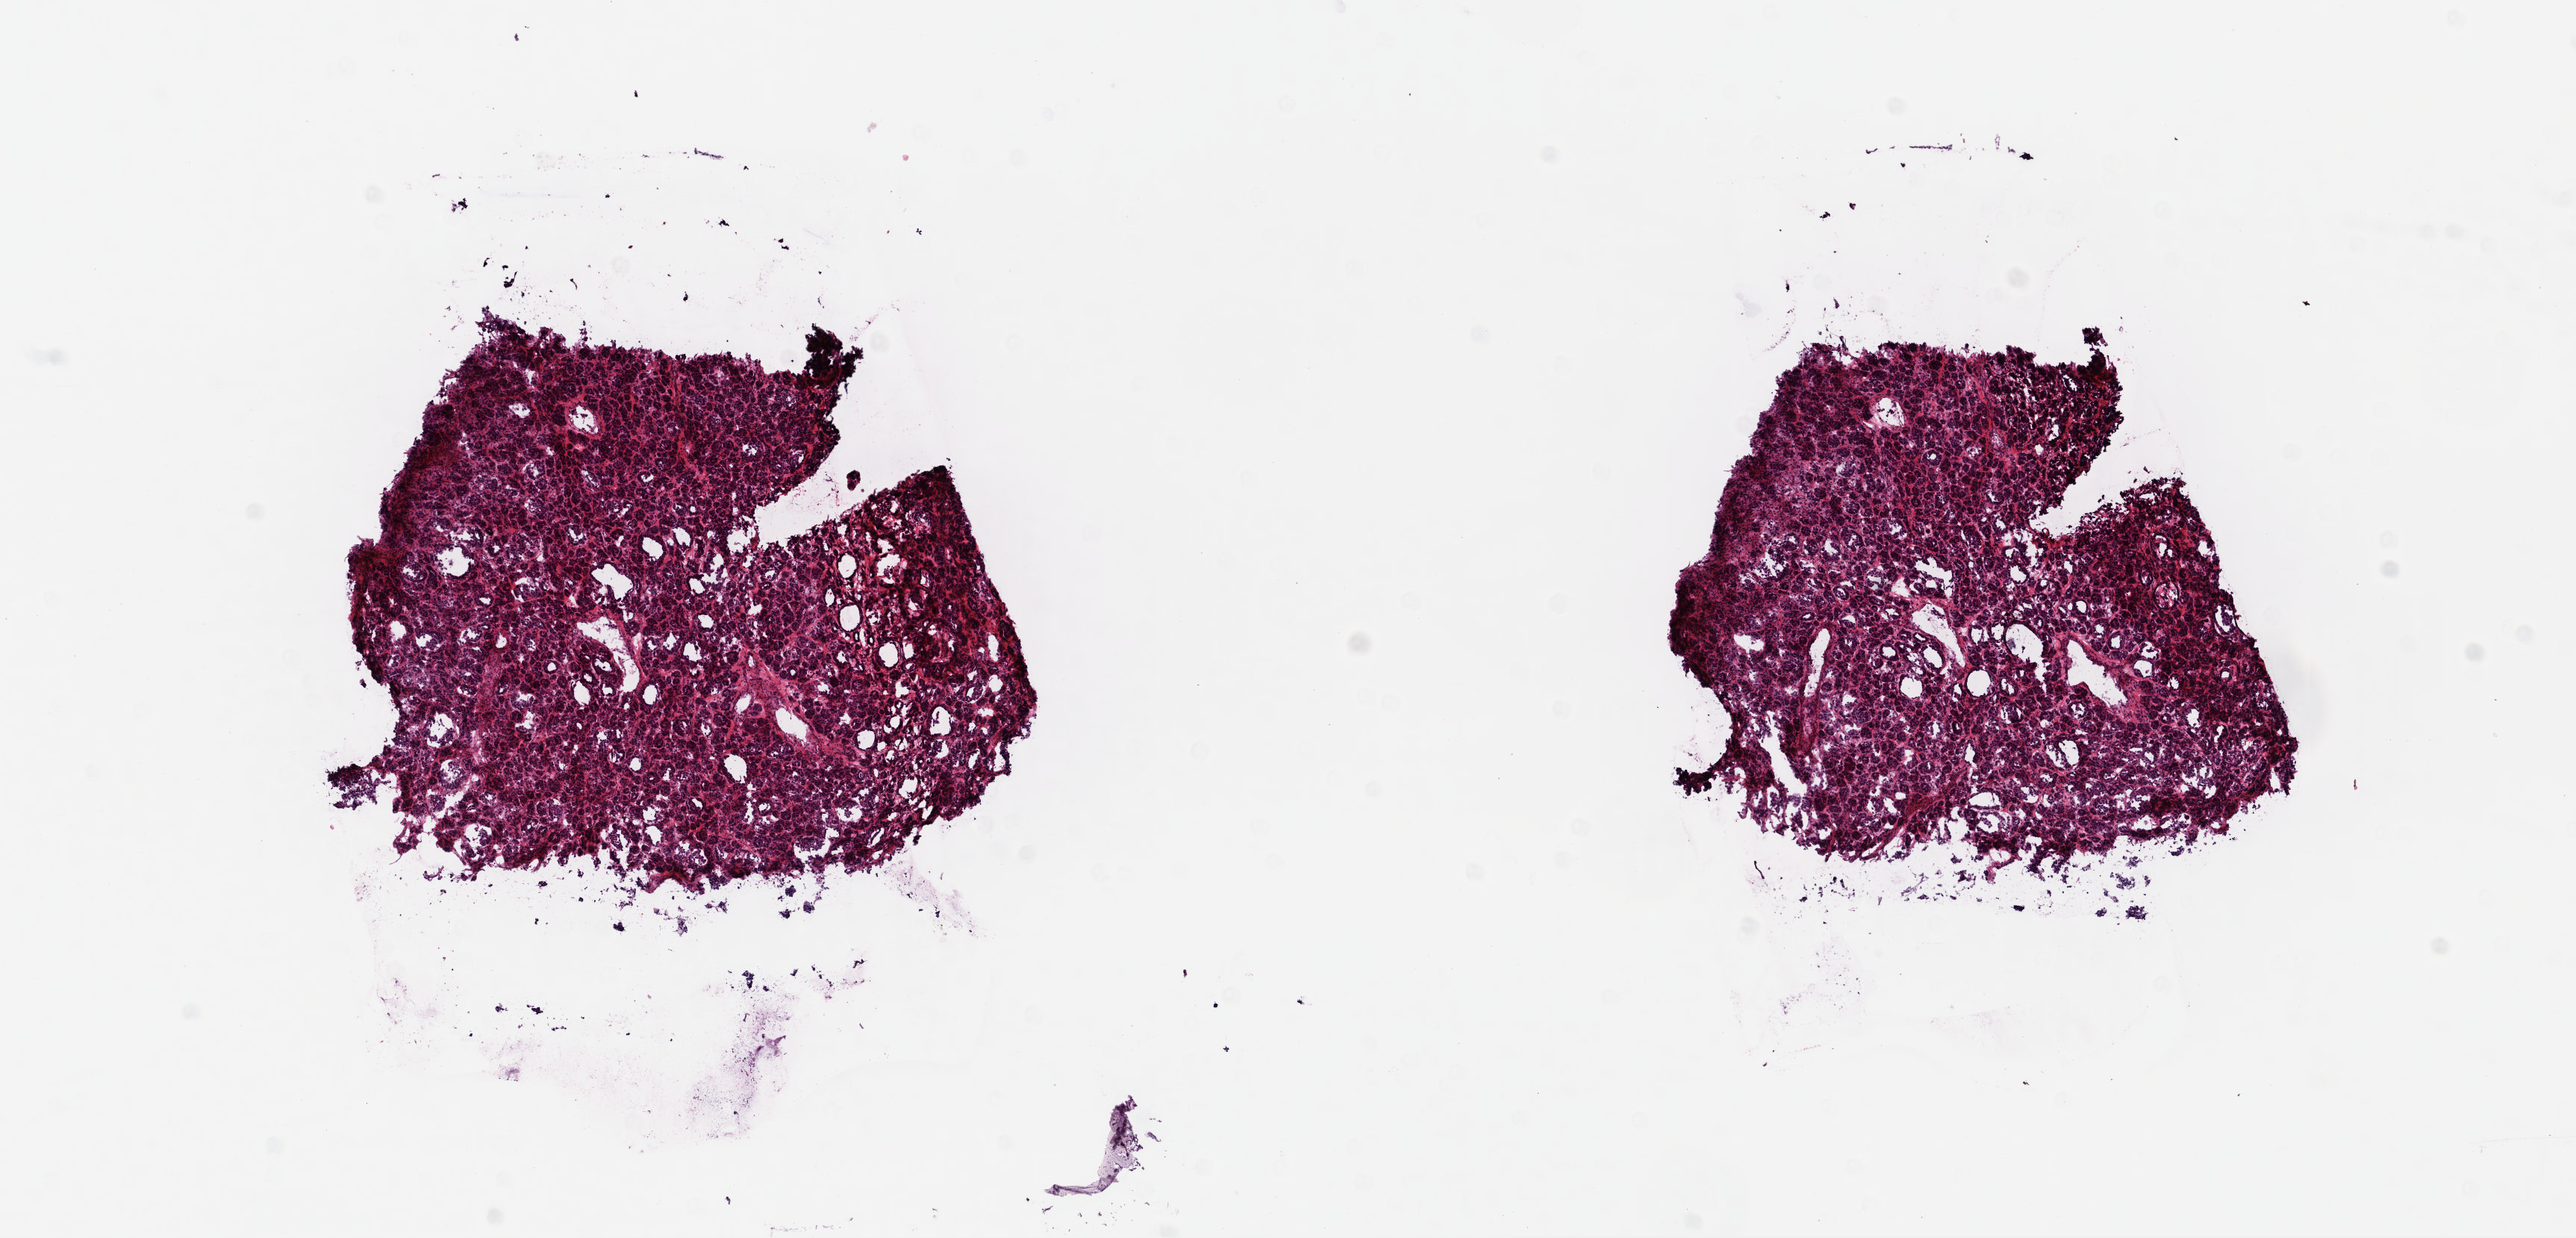
Hematoxylin and eosin (H&E) stained whole-slide image — whole scanned area (about 13.6 x 6.5 mm) shown as a low-resolution overview; frozen section; primary tumour sample from the thyroid. Patient: female, age at initial diagnosis 47 years. Pathologist review of this section (percent, as recorded): tumour cells 90%, tumour nuclei 95%.
Diagnosis: Papillary carcinoma, follicular variant (thyroid gland).